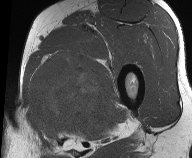
MRI of an extremity soft-tissue mass, one axial slice; position 37 of 61 along the scan axis; MR volume resampled by the dataset authors to the PET/CT grid (not the native acquisition matrix); 192 × 158 image matrix, field of view 187 × 154 mm. Male patient. From the clinical record (not read from this slice): histological type: pleiomorphic liposarcoma; grade: high; site of the primary tumour: left thigh.
Annotated regions visible in this slice (expert contour drawn on MRI and transferred to this co-registered scan by the dataset authors):
- gross tumour volume including surrounding oedema: bounding box (x1, y1, x2, y2) in pixels: (29, 50, 110, 141)
- gross tumour volume (mass): (29, 53, 110, 129)